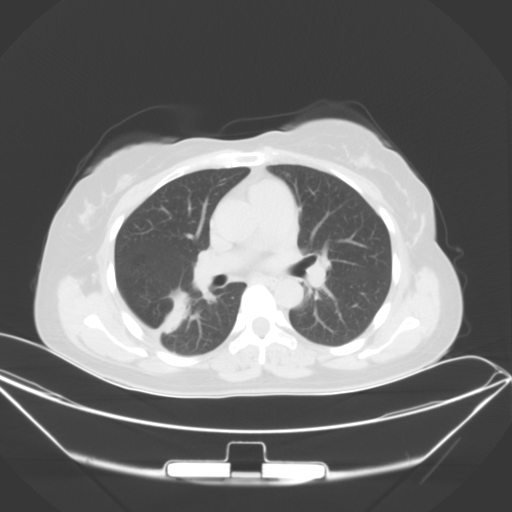
Chest CT, one axial slice; slice 23 of 46 in the series (ordered by position); 120 kVp; lung window (W 1500 / L -600 HU); 5 mm slice thickness; 512 × 512 image matrix, field of view 407 × 407 mm. Patient: female, 42 years. Case-level facts recorded for this patient, not image findings: clinical TNM (as recorded): T1c N0 M1a.
Annotated regions visible in this slice (bounding box drawn by a radiologist):
- lung tumour (recorded histology: adenocarcinoma): bounding box <150,286,198,339> (left, top, right, bottom; pixels)